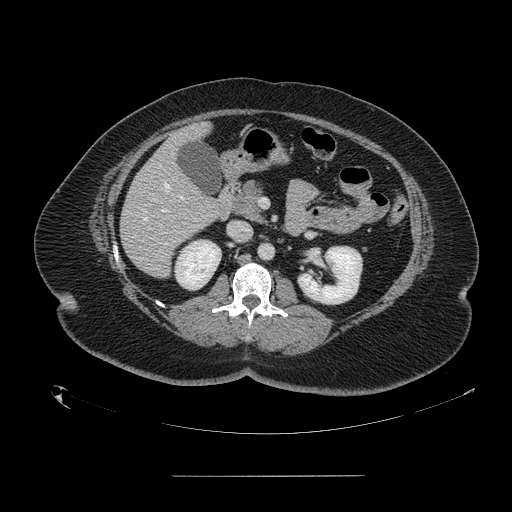
Contrast-enhanced abdominal CT, one axial slice. Position 68 of 164 along the scan axis. Intravenous contrast given. Soft-tissue window (W 400 / L 40 HU). 2.5 mm slice thickness. 512 × 512 image matrix, field of view 495 × 495 mm. Female patient, age 52 years. Case-level facts recorded for this patient, not image findings: diagnosis: colorectal cancer liver metastases, imaged before liver resection; multiple liver metastases: yes; largest metastasis: 3.5 cm; disease in both lobes: no.
Outlined on this slice (manually delineated by an expert):
- hepatic veins: bounding box (x1, y1, x2, y2) in pixels: (142, 183, 169, 221)
- liver: (121, 125, 230, 277)
- planned liver remnant (the part of the liver to remain after resection): (182, 125, 209, 142)
- portal vein (with intrahepatic branches): (179, 196, 182, 199)